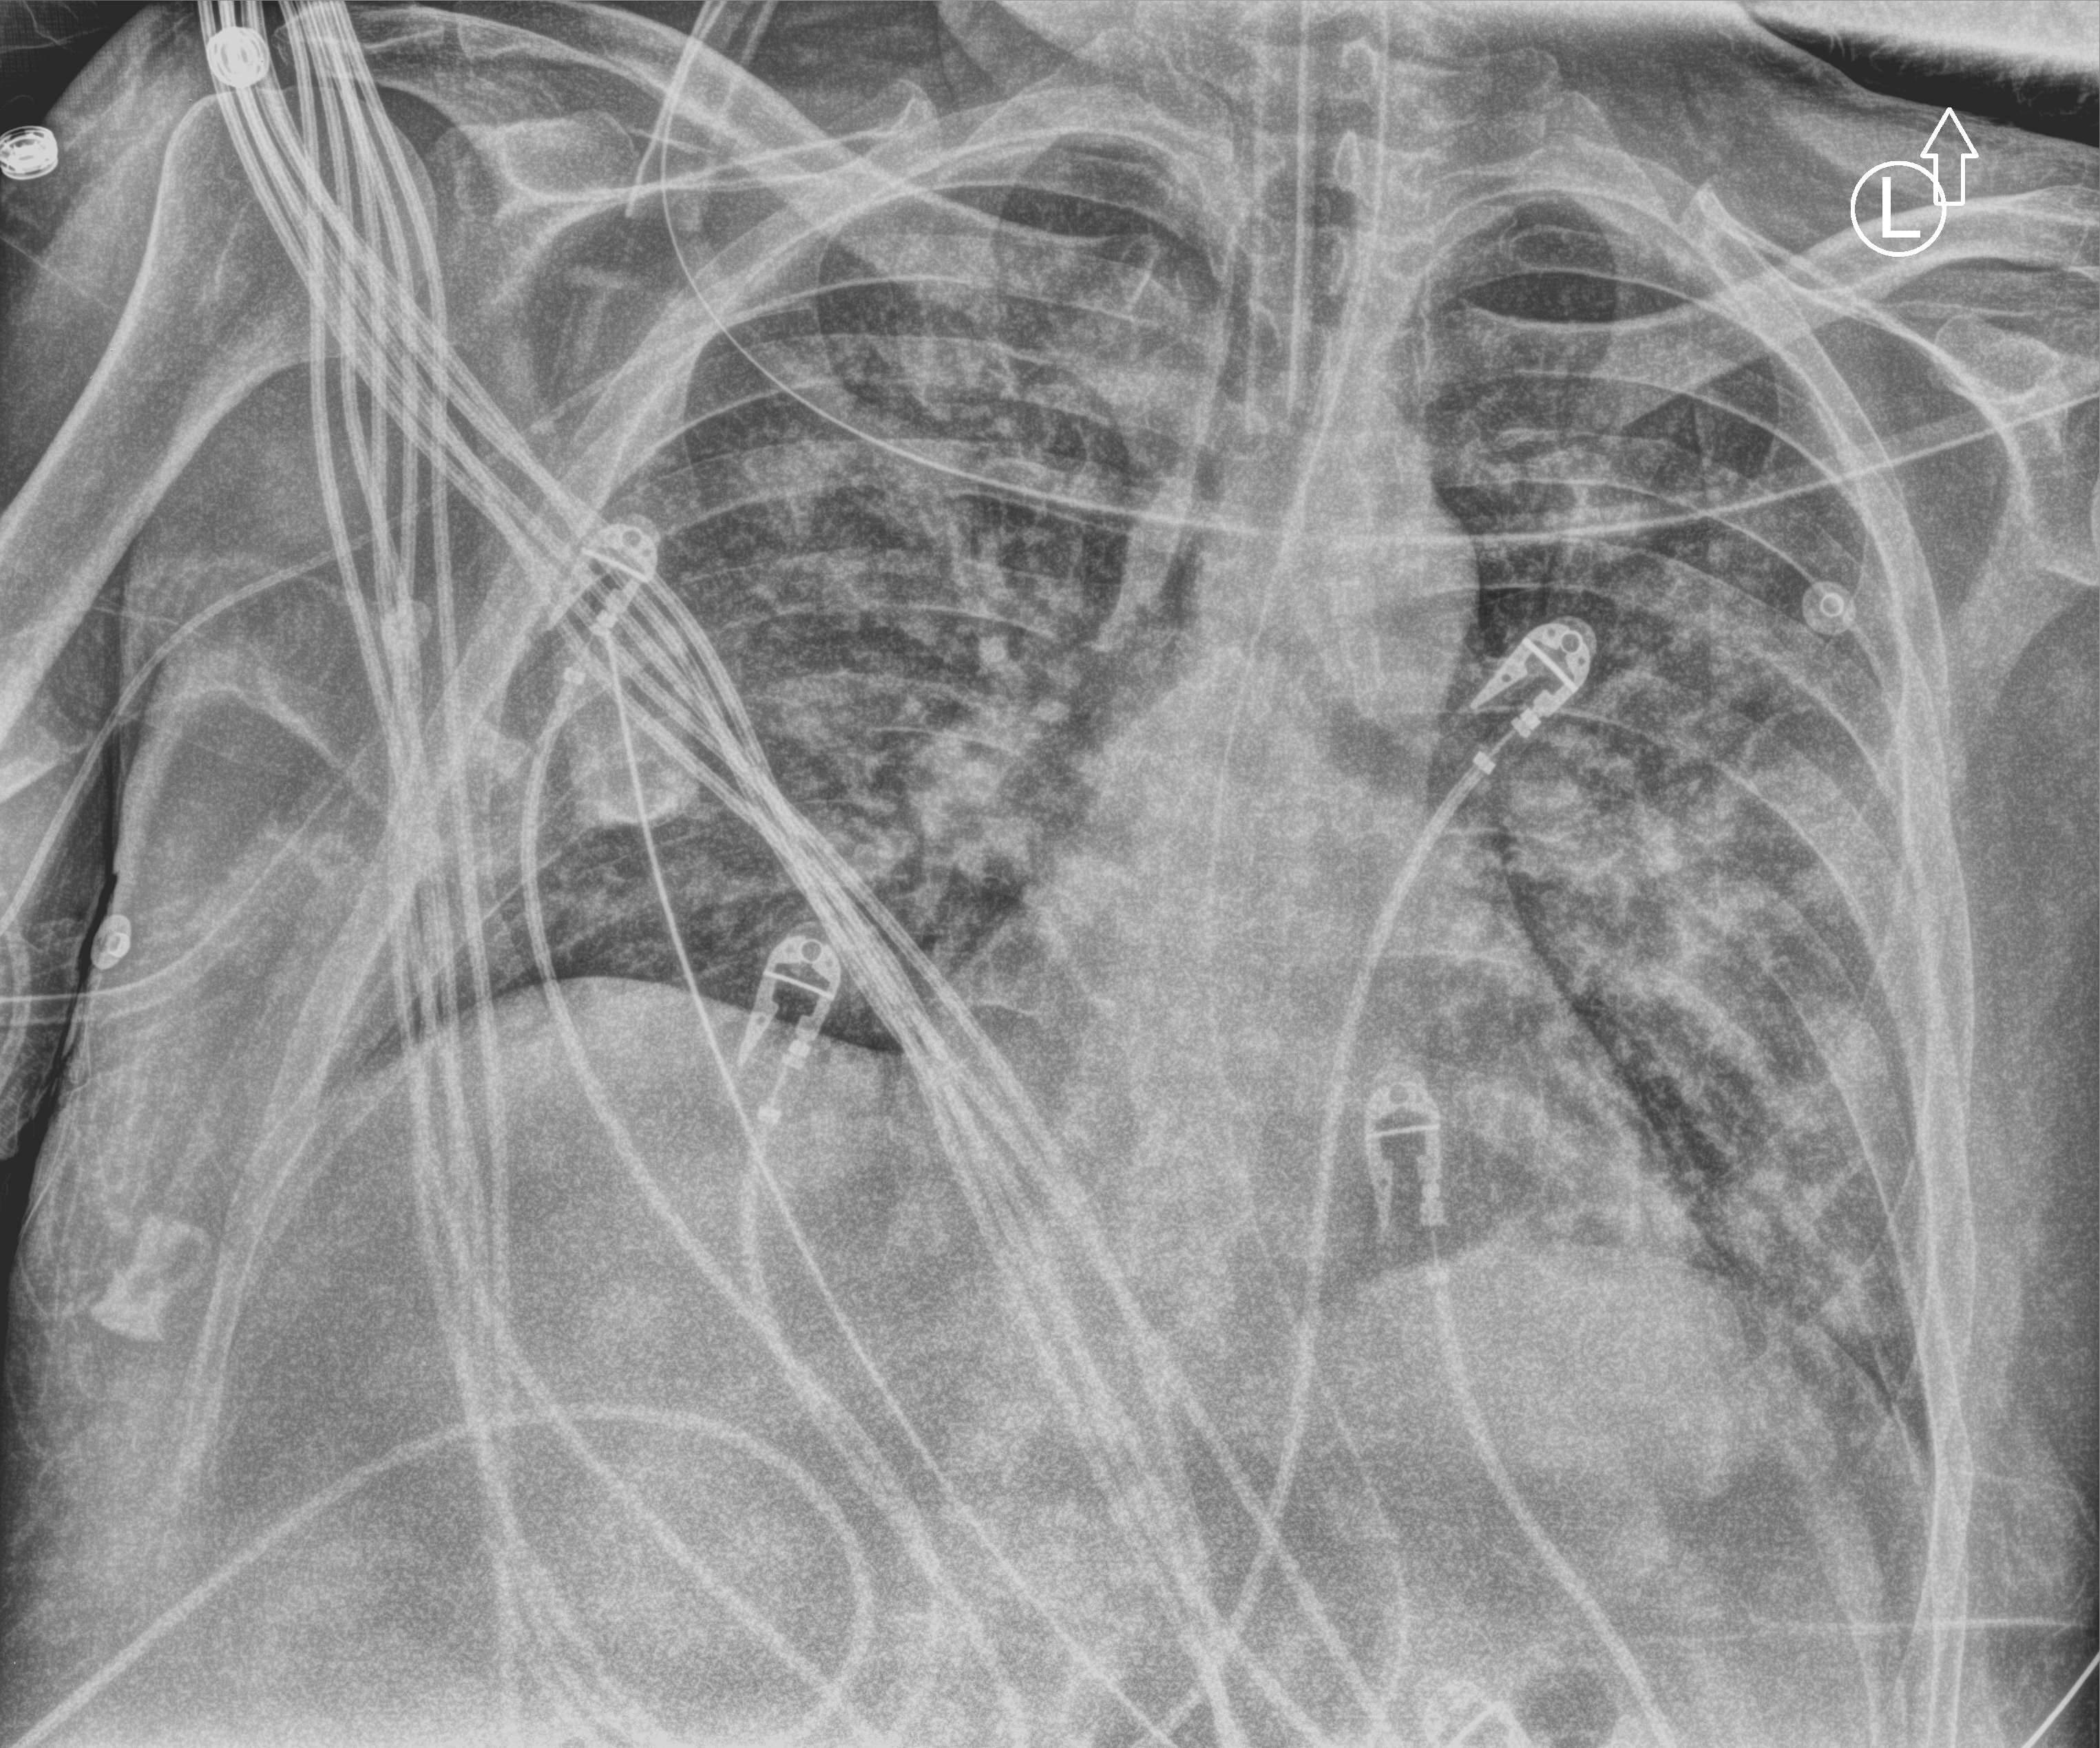
Portable chest radiograph; anteroposterior (AP) projection. Male patient hospitalised with COVID-19, age 18–59 years.
From the hospital-stay record, not from the radiograph (when in the stay this image was taken is not recorded): mechanically ventilated during this hospital stay: yes; length of hospital stay: 20 days.